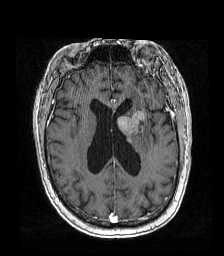
Brain MRI from a brain-tumour surgery series, one axial slice; slice 71 of 192 in the series (ordered by position); T1-weighted post-contrast; 224 × 256 image matrix, field of view 219 × 250 mm. Case-level facts recorded for this patient, not image findings: histopathology: Metastatic carcinoma from lung primary.
Outlined on this slice (outlined manually by an expert reader):
- tumour: bounding box [x1, y1, x2, y2] px = [117, 110, 148, 145]